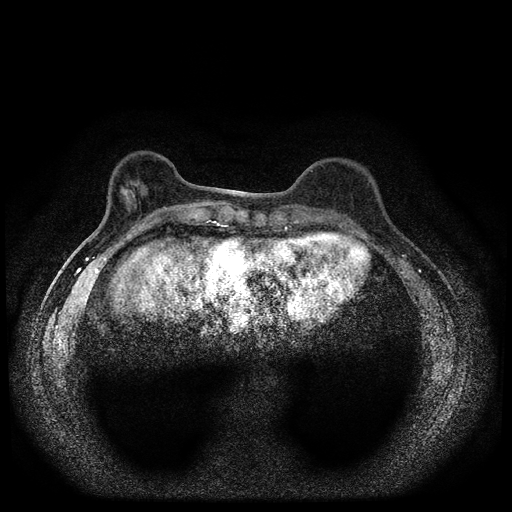
Breast MRI (dynamic contrast-enhanced, multi-phase), one axial slice. Position 28 of 112 along the scan axis. Dynamic contrast-enhanced series, time point 2 of 5 at this slice position (early post-contrast). 1.5 T. TE 2.7 ms, TR 5.4 ms. 2 mm slice thickness. 512 × 512 image matrix, field of view 320 × 320 mm. Patient: female, 61 years.
Outlined on this slice (semi-automatically segmented with operator editing):
- breast lesion (labelled benign in the annotation): box from (x=120, y=179) to (x=139, y=204) px